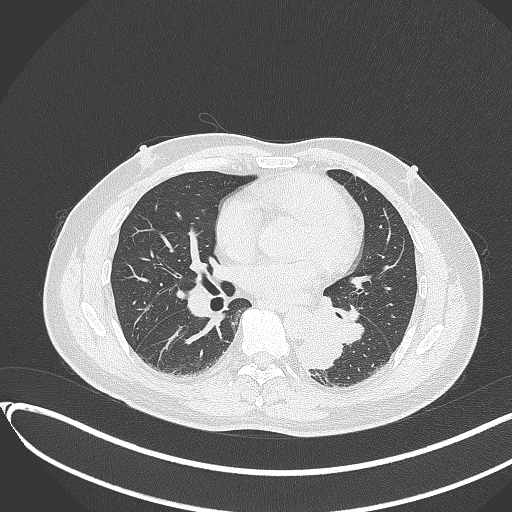
Chest CT, one axial slice; position 162 of 417 along the scan axis; reconstruction kernel B70f; 120 kVp; lung window (W 1500 / L -600 HU); 1 mm slice thickness; 512 × 512 image matrix. Male patient, age 54 years. Case-level facts recorded for this patient, not image findings: clinical TNM (as recorded): T3 N0 M0.
Outlined on this slice (bounding box drawn by a radiologist):
- lung tumour (recorded histology: squamous cell carcinoma): box from (x=296, y=325) to (x=347, y=370) px